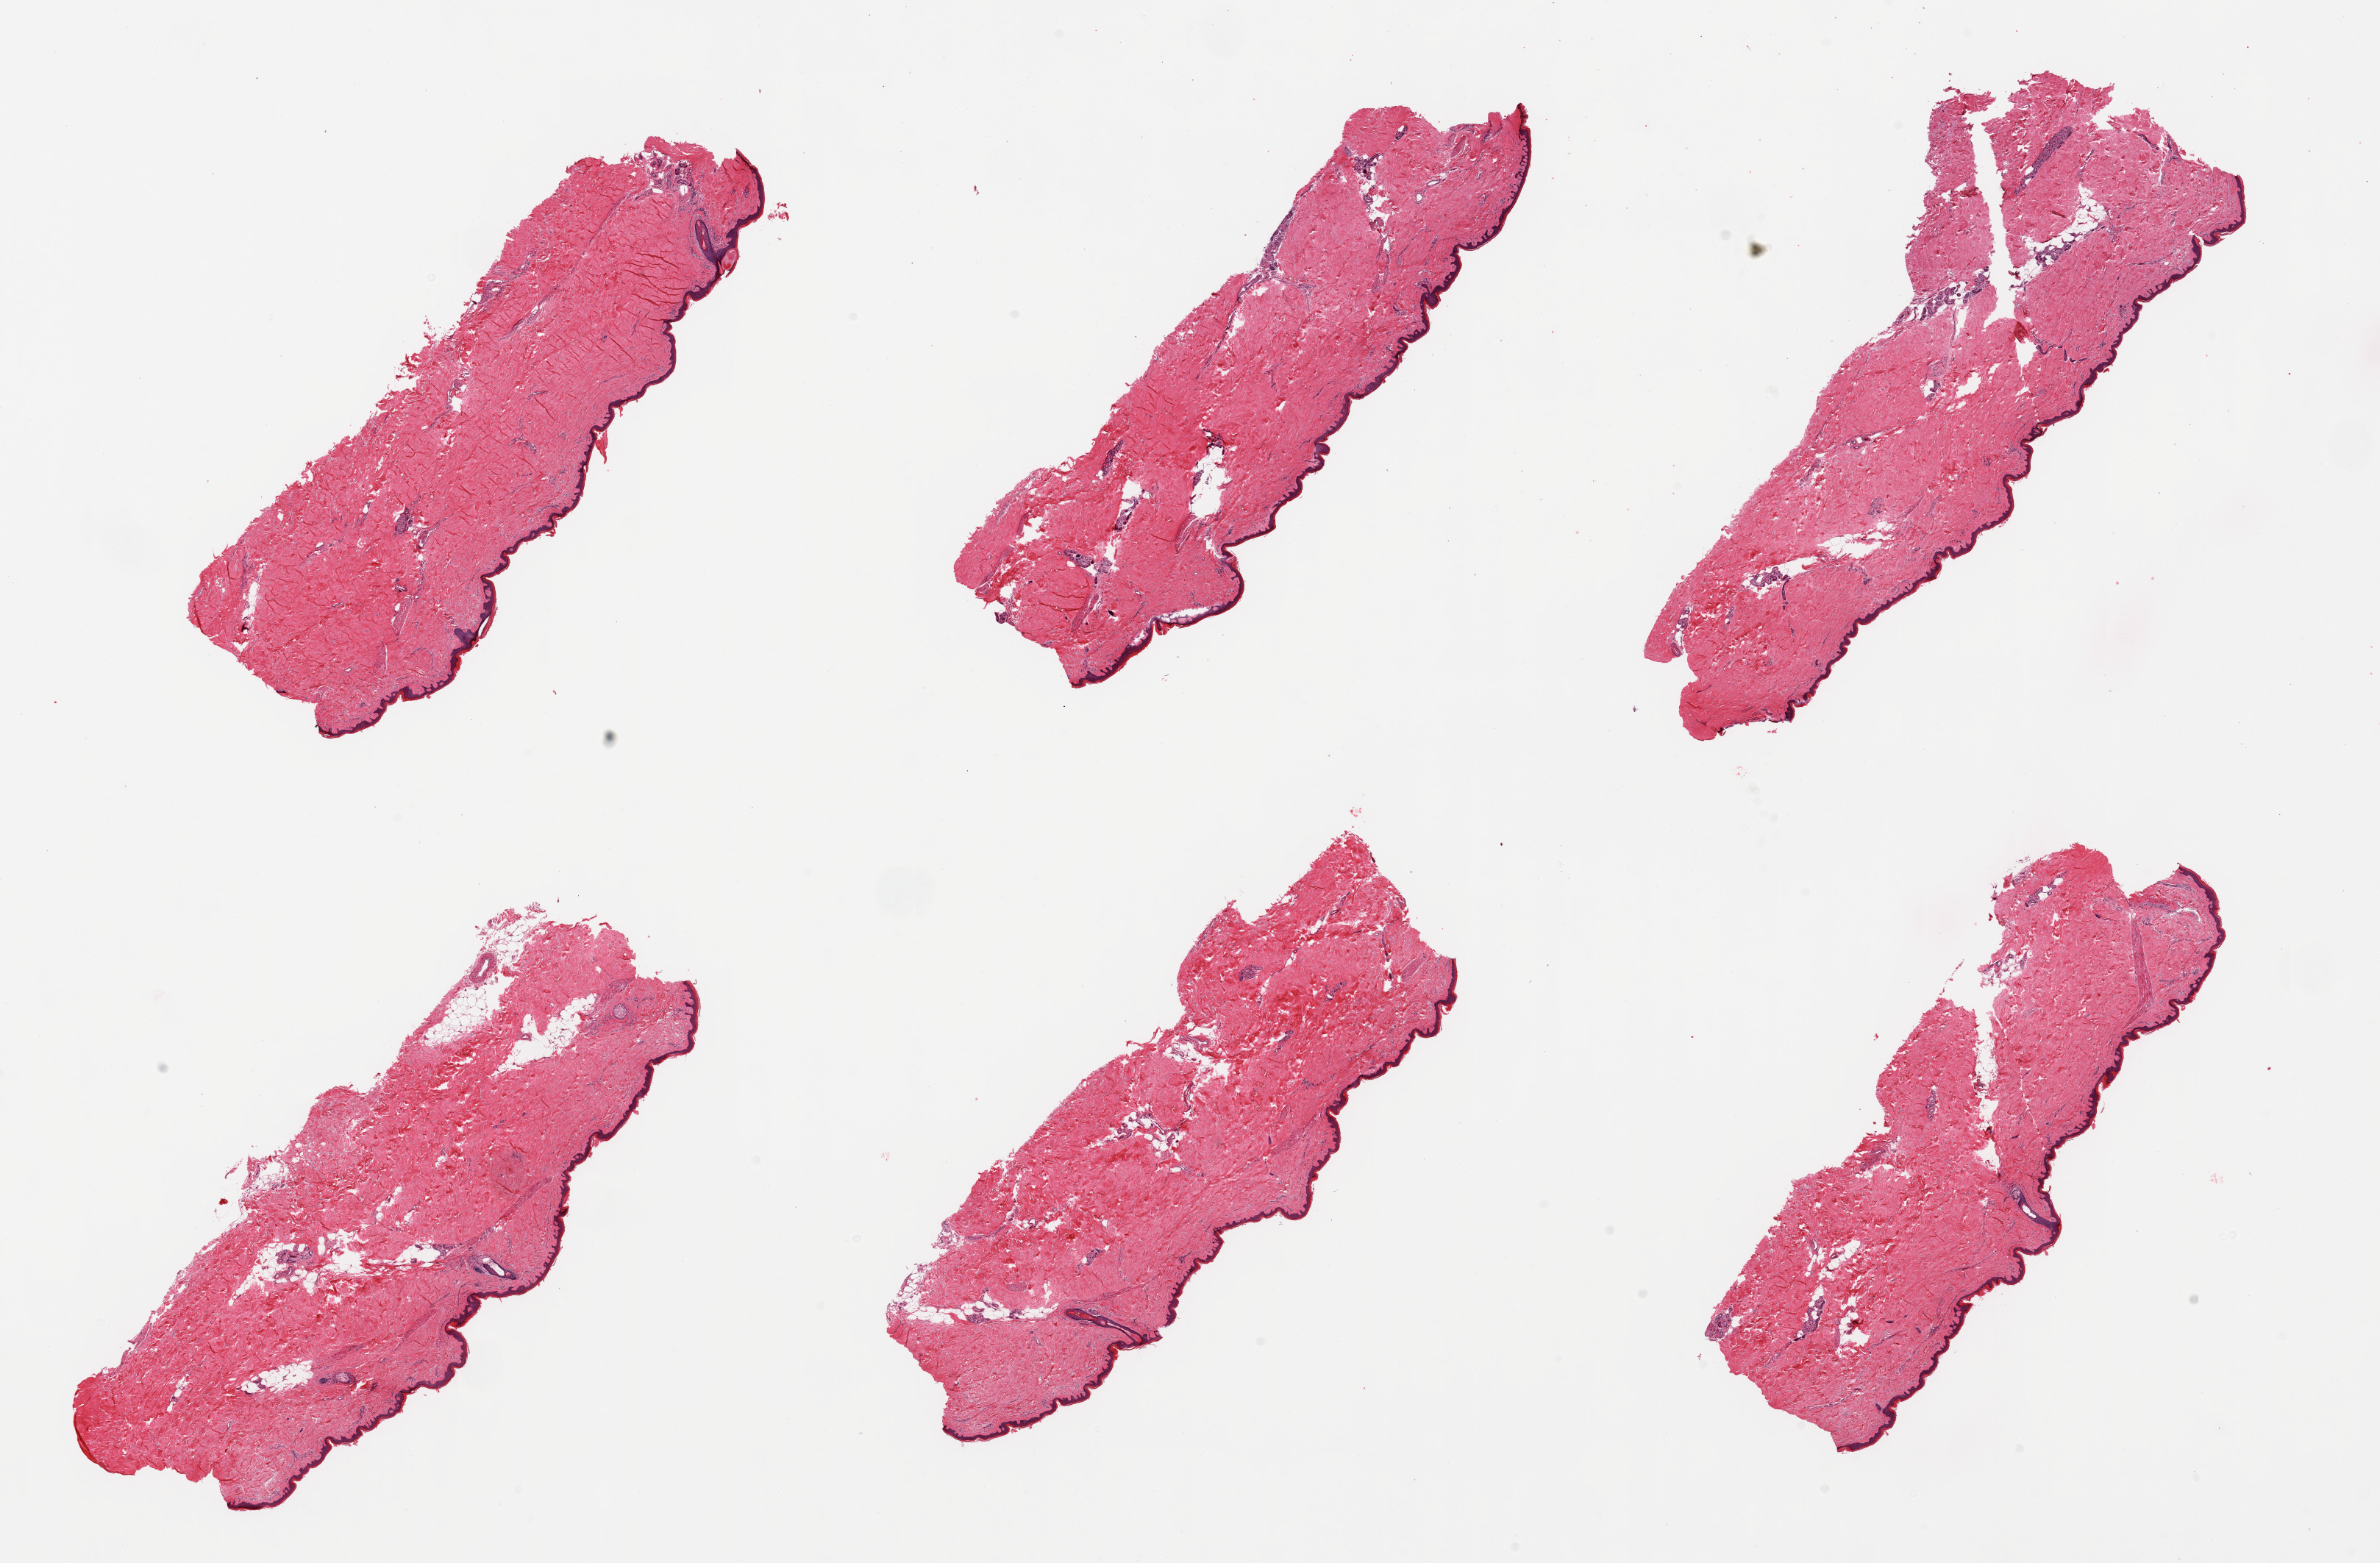
H&E whole-slide image — whole scanned area (about 25.6 x 16.8 mm) shown as a low-resolution overview, PAXgene-fixed, paraffin-embedded tissue, sampled site (target tissue): skin of lower leg, tissue donor sample. Donor sex: male.
Review note (as recorded): 6 pieces; 5% internal (periadnexal) fat; epidermis ~31 microns.